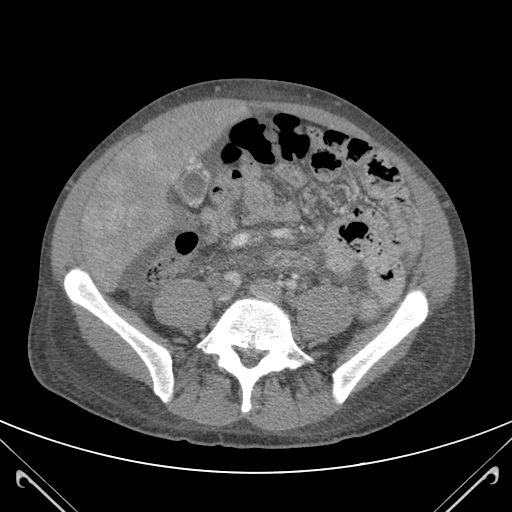
Contrast-enhanced abdominal CT (liver protocol), one axial slice; position 26 of 118 along the scan axis; 120 kVp; soft-tissue window (W 400 / L 40 HU); 3 mm slice thickness; 512 × 512 image matrix, field of view 380 × 380 mm. Case-level facts recorded for this patient, not image findings: diagnosis: hepatocellular carcinoma (patient treated with transarterial chemoembolisation; whether this scan precedes or follows treatment is not stated here); TNM stage (as recorded): Stage-IIIB; Child-Pugh class: A.
Structures marked on this image (semi-automatically segmented with operator editing):
- mass: bounding box (x1, y1, x2, y2) in pixels: (84, 126, 188, 269)